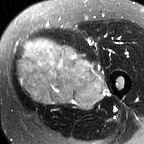
MRI of an extremity soft-tissue mass, one axial slice; slice 26 of 60 in the series (ordered by position); T2-weighted fat-saturated; MR volume resampled by the dataset authors to the PET/CT grid (not the native acquisition matrix); 3.27 mm slice thickness; 144 × 144 image matrix. Female patient. From the clinical record (not read from this slice): histological type: pleiomorphic leiomyosarcoma; grade: intermediate; site of the primary tumour: left thigh.
Outlined on this slice (expert contour drawn on MRI and transferred to this co-registered scan by the dataset authors):
- gross tumour volume including surrounding oedema: box from (x=15, y=38) to (x=110, y=111) px
- gross tumour volume (mass): (x=15, y=38)–(x=105, y=109)